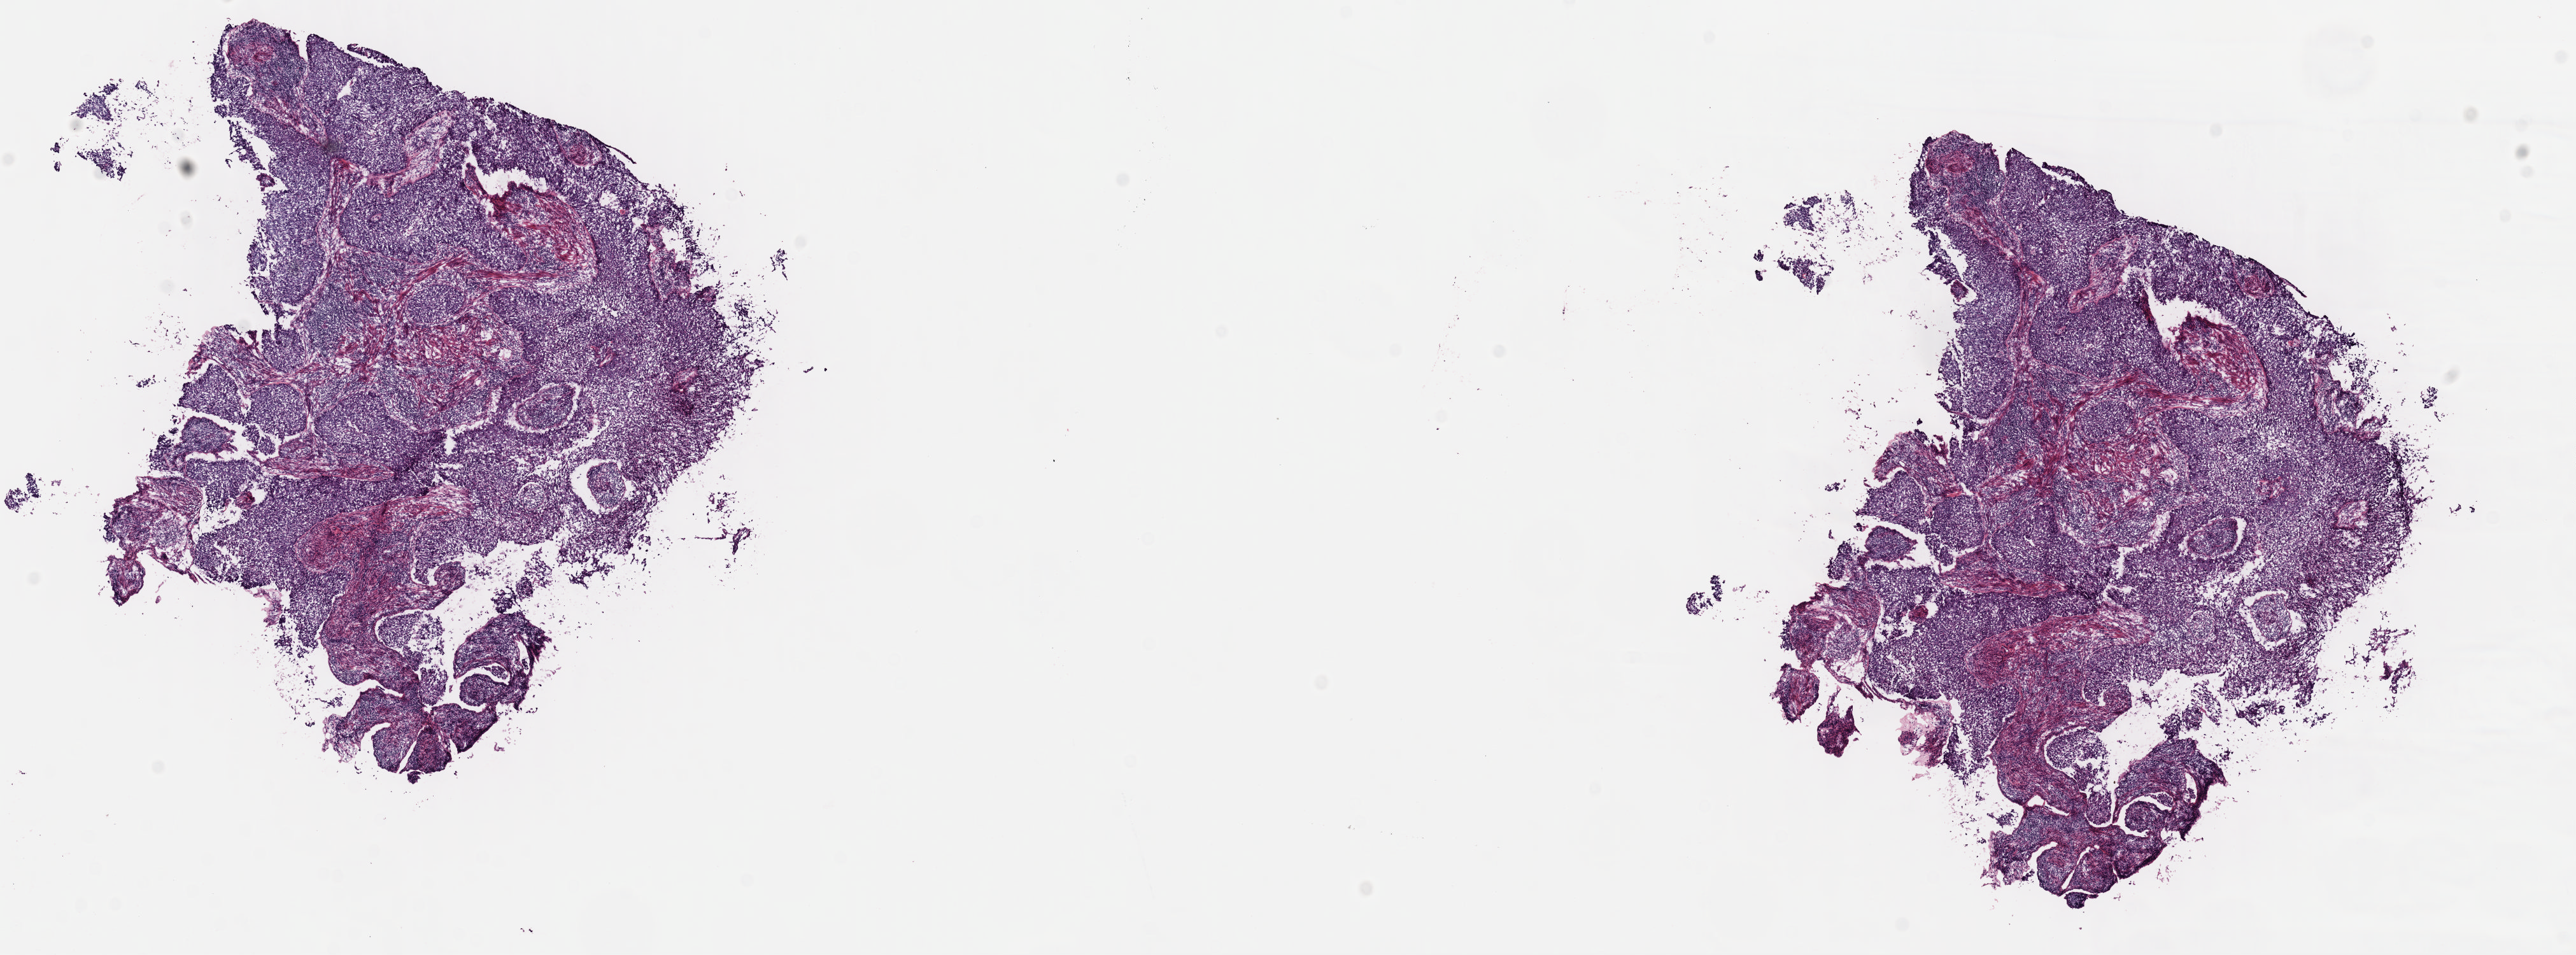
Digitized Hematoxylin and eosin (H&E) stained tissue section (whole slide), a low-resolution overview of the entire scanned area, about 16.0 x 5.9 mm; frozen section; primary tumour sample from the cervix. Patient: female, age at initial diagnosis 74 years. Histologic grade: G3 (poorly differentiated). Slide review estimates, as recorded: tumour cells 60%, tumour nuclei 65%, normal cells 15%, stromal cells 22%, necrosis 3%. Inflammatory infiltration, as recorded: lymphocyte infiltration 25%, monocyte infiltration 0%, neutrophil infiltration 0%.
Histologic diagnosis: Squamous cell carcinoma, large cell, nonkeratinizing, NOS (cervix uteri). FIGO stage: IIA2. Lymph nodes positive (case pathology): 0 of 32 examined.